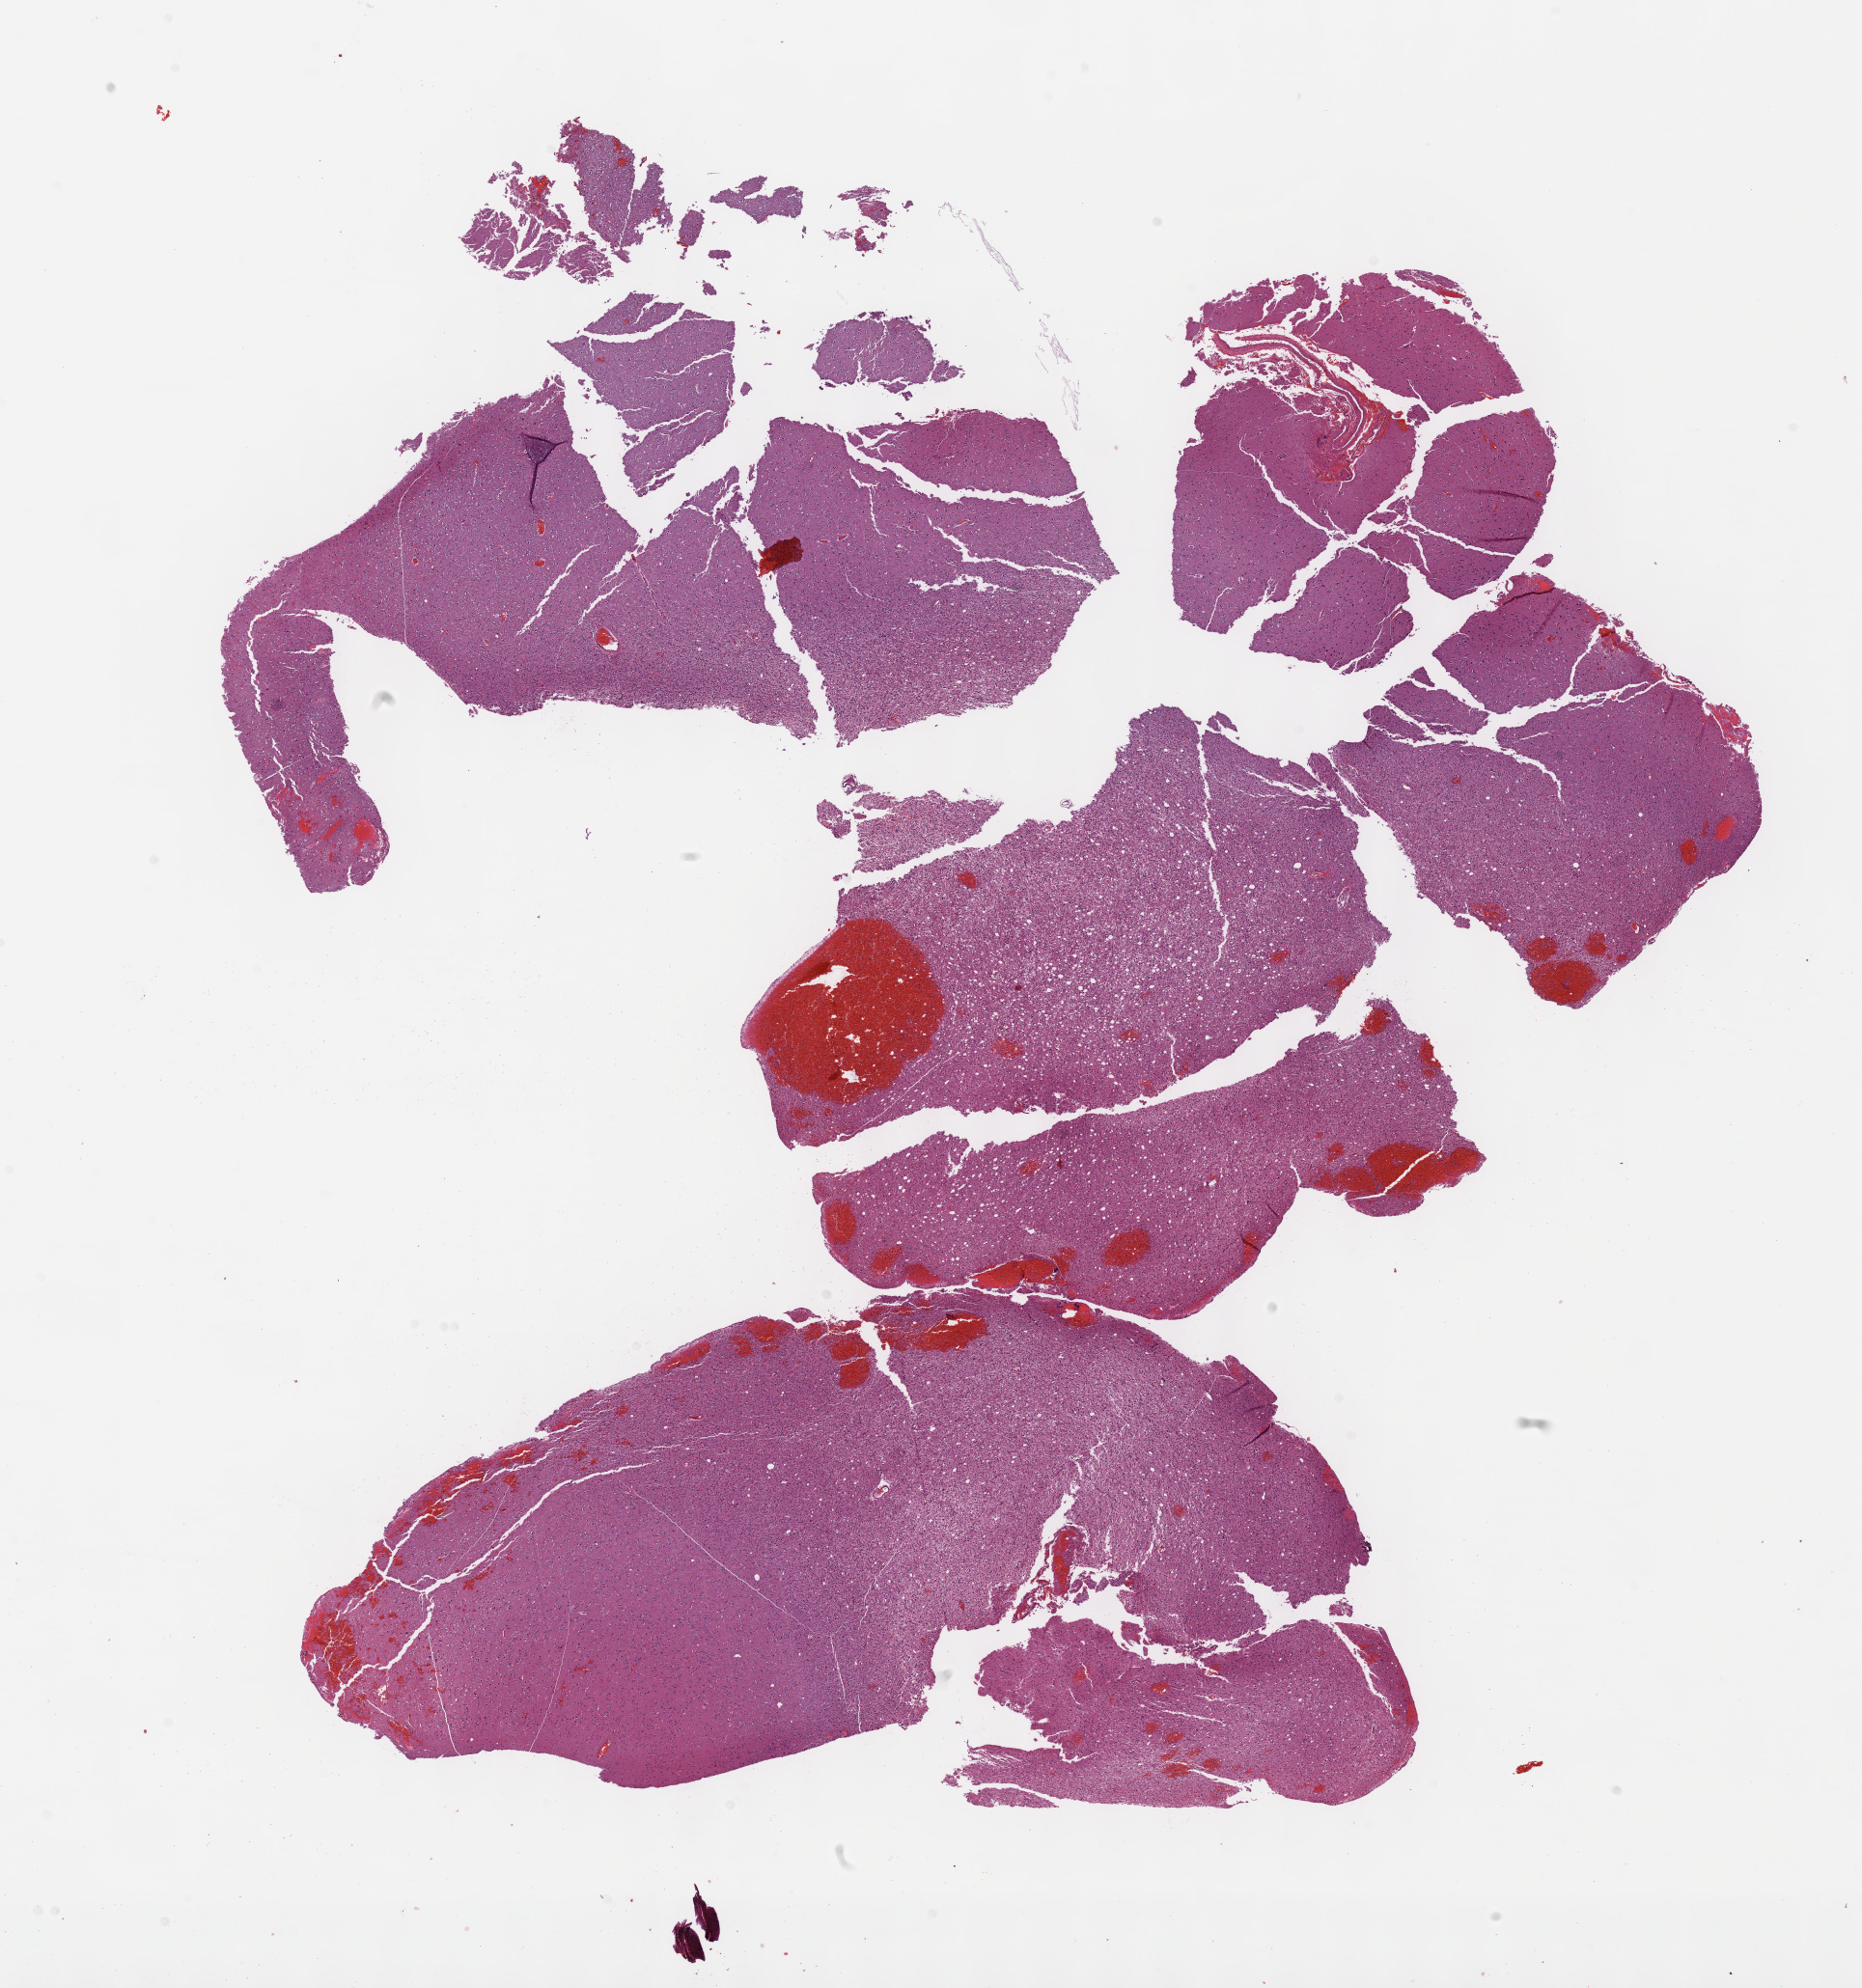
H&E whole-slide image, shown as a low-resolution overview of the whole scanned area (about 15.6 x 16.7 mm), FFPE section, brain, primary tumour sample. Patient: female, age at initial diagnosis 29 years. Histologic grade: G2 (moderately differentiated).
• laterality: right
• diagnosis: Mixed glioma (cerebrum)